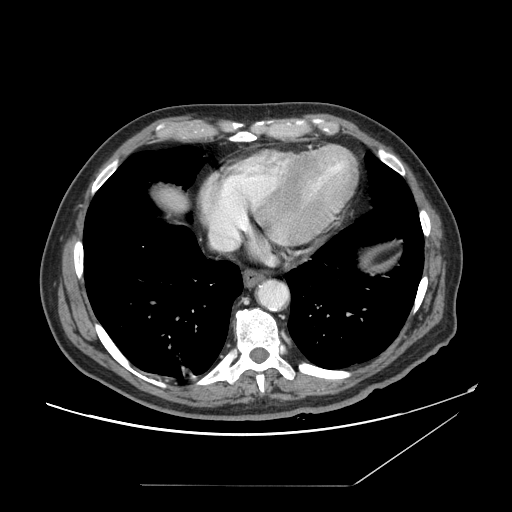
Contrast-enhanced abdominal CT, one axial slice; position 146 of 166 along the scan axis; 120 kVp; soft-tissue window (W 400 / L 40 HU); 512 × 512 image matrix, field of view 416 × 416 mm. Male patient, age 80 years. Case-level facts recorded for this patient, not image findings: diagnosis: colorectal cancer liver metastases, imaged before liver resection; multiple liver metastases: no; largest metastasis: 2.2 cm; disease in both lobes: no.
Structures marked on this image (expert manual segmentation):
- liver: bounding box <154,187,190,212> (left, top, right, bottom; pixels)
- planned liver remnant (the part of the liver to remain after resection): <153,186,190,212>